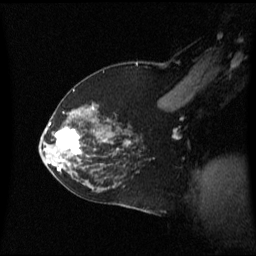
Breast MRI (dynamic contrast-enhanced), one sagittal slice; slice 41 of 60 in the series (ordered by position); dynamic contrast-enhanced series, image 2 of 3 at this slice position (ordered by acquisition); 1.5 T; TE 4.2 ms, TR 8.4 ms; 256 × 256 image matrix. Female patient, age 59 years. From the clinical record (not read from this slice): setting: breast cancer imaged before/during neoadjuvant chemotherapy; receptor status: HR-positive, HER2-negative.
Outlined on this slice (semi-automatic segmentation, software-assisted and operator-edited):
- analysis volume of interest (the breast-tissue region the enhancement analysis was run in; not a lesion): bounding box (x1, y1, x2, y2) in pixels: (46, 114, 89, 163)
- tumour enhancement mask (voxels above the 70 % enhancement threshold inside the analysis volume of interest): (55, 128, 81, 155)